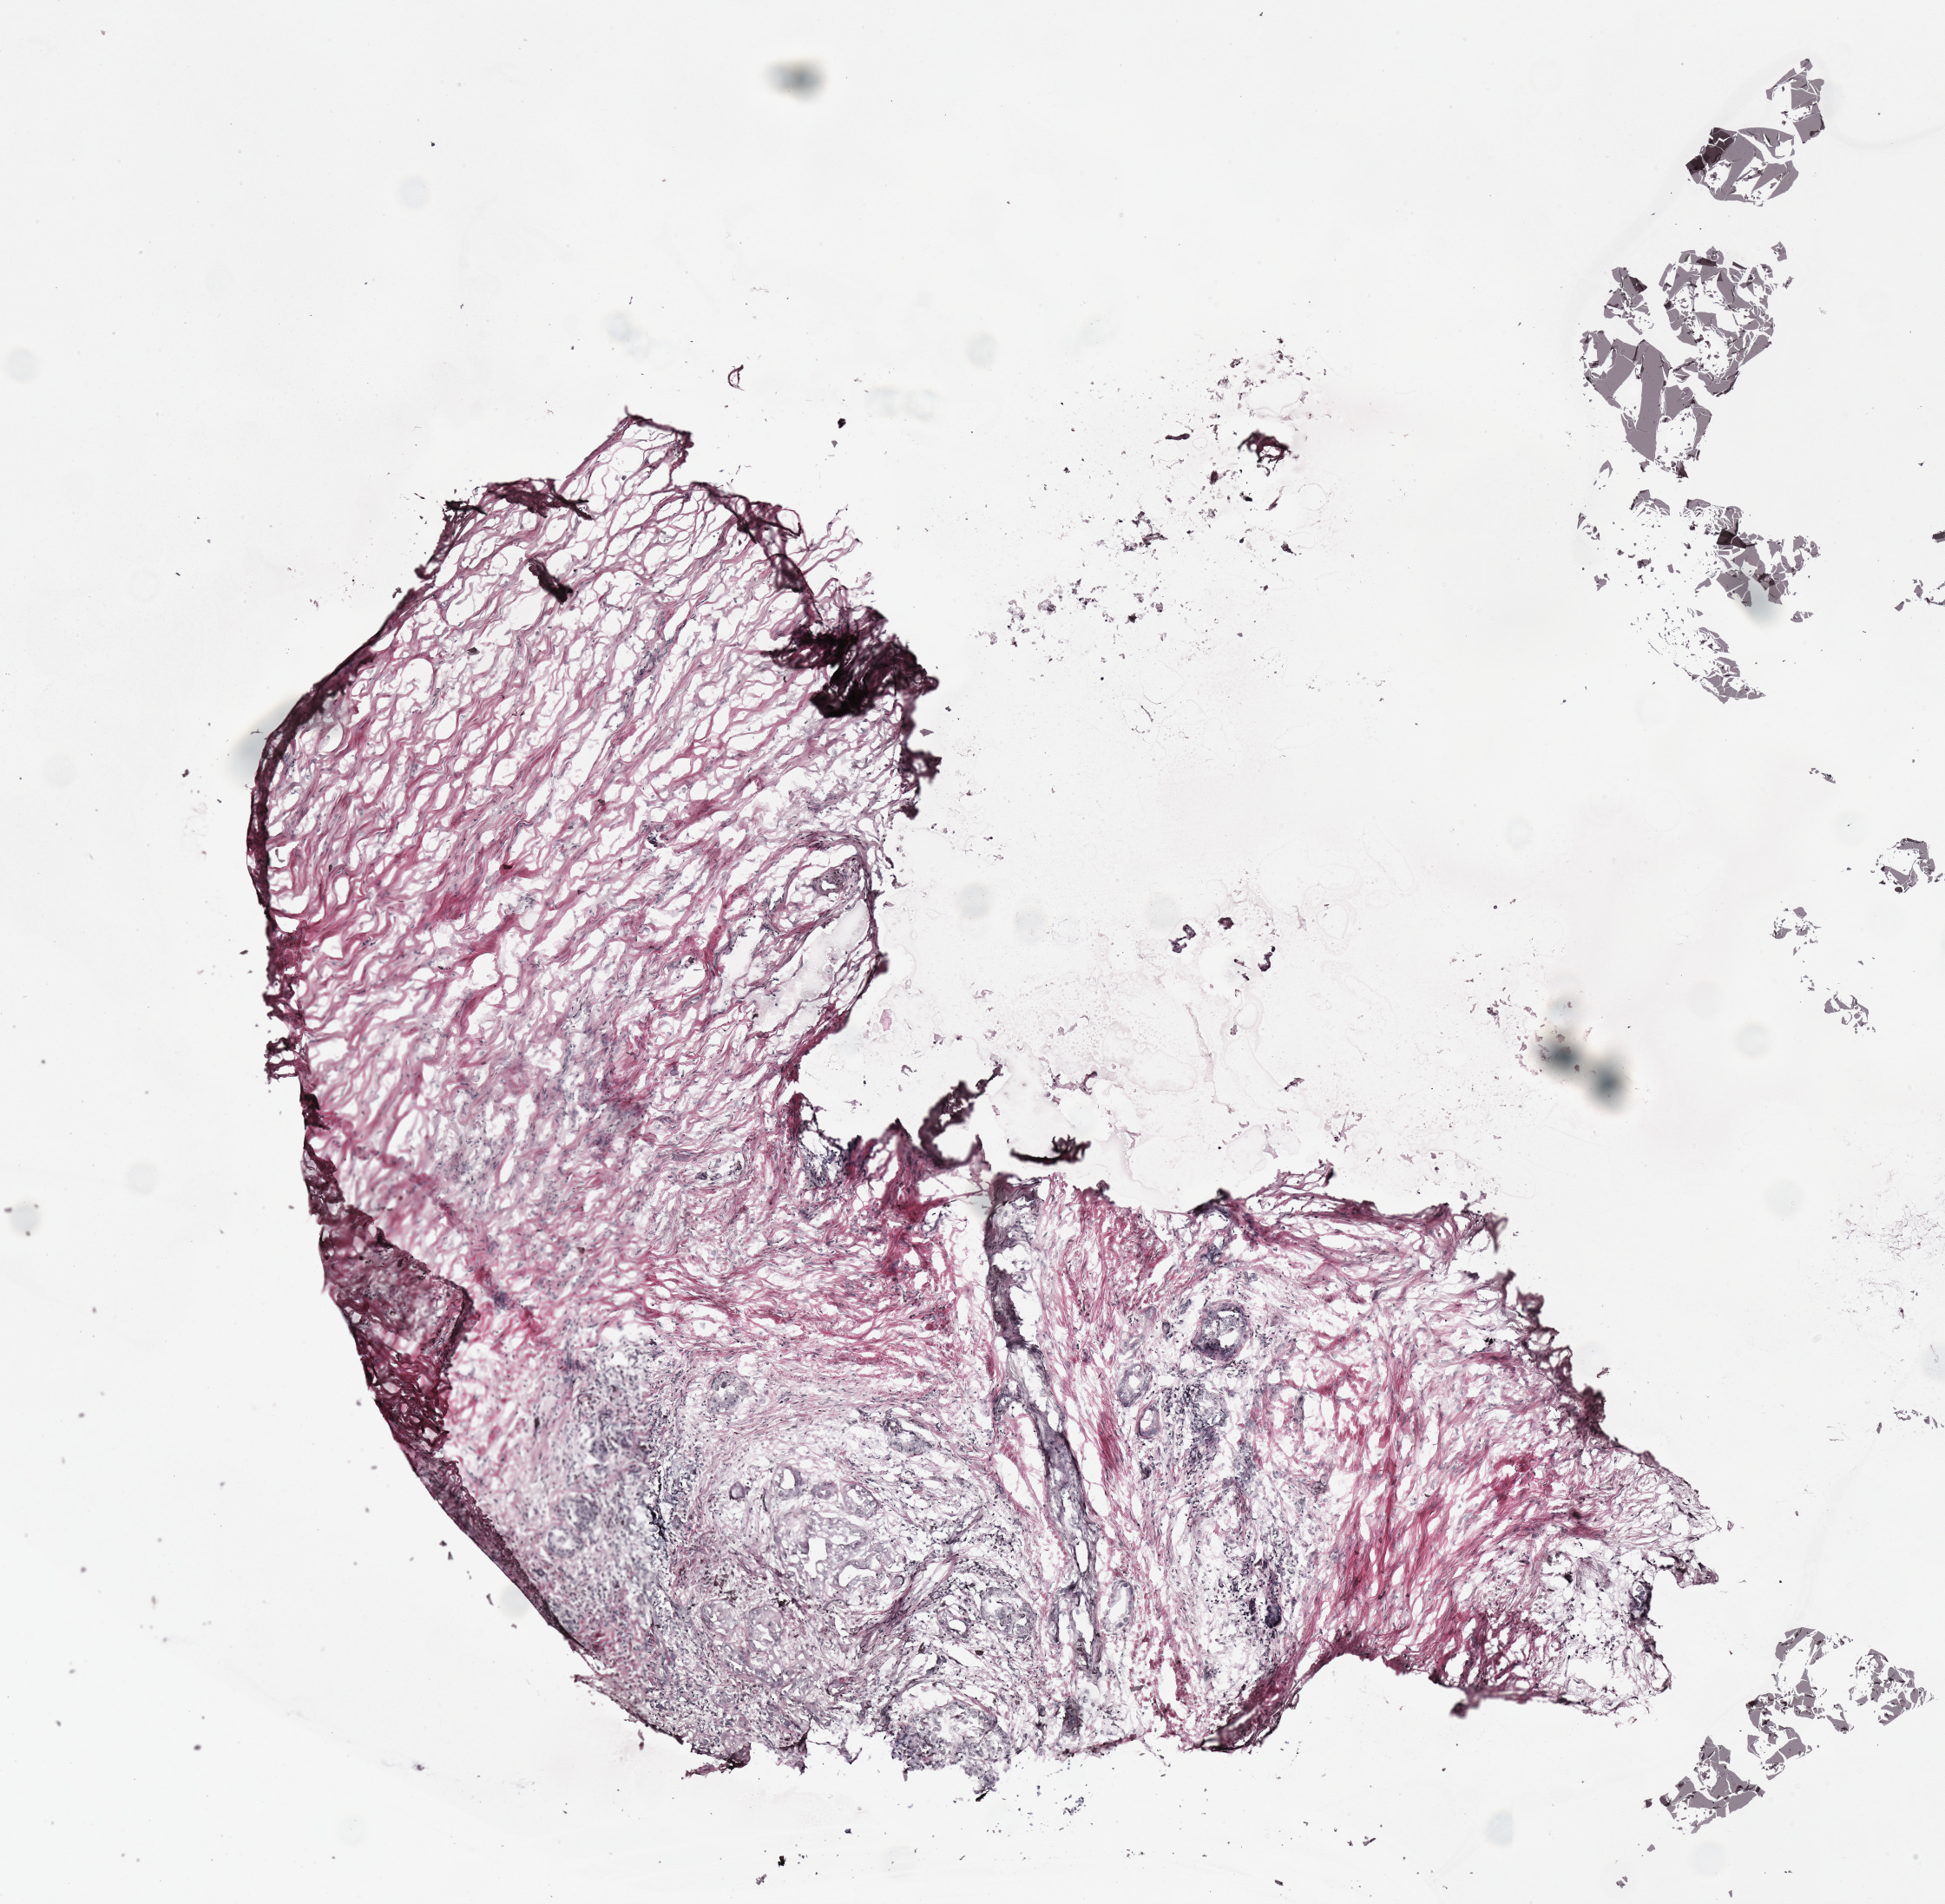
Hematoxylin and eosin (H&E) stained whole-slide image — shown as a low-resolution overview of the whole scanned area (about 4.4 x 4.3 mm), frozen section, sample: primary tumour, pancreas. Male, age 64 years at initial diagnosis. Histologic grade: G3 (poorly differentiated). Slide review estimates, as recorded: tumour cells 40%, tumour nuclei 50%, normal cells 0%, stromal cells 60%, necrosis 0%.
Pathologic diagnosis: Infiltrating duct carcinoma, NOS. AJCC pathologic stage: IIA. Lymph nodes positive (case pathology): 0 of 8 examined.